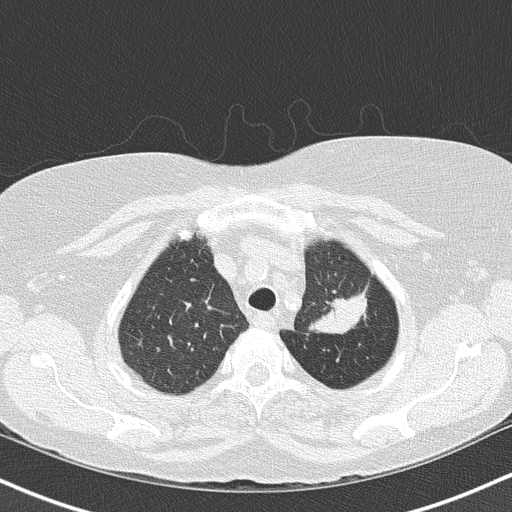
Low-dose screening chest CT, one axial slice. Position 124 of 147 along the scan axis. 120 kVp. Lung window (W 1500 / L -600 HU). 512 × 512 image matrix, field of view 320 × 320 mm.
Annotated regions visible in this slice (outlined manually by an expert reader):
- lesion 1 (tumor, upper lobe of left lung): bounding box (x1, y1, x2, y2) in pixels: (311, 294, 366, 334)